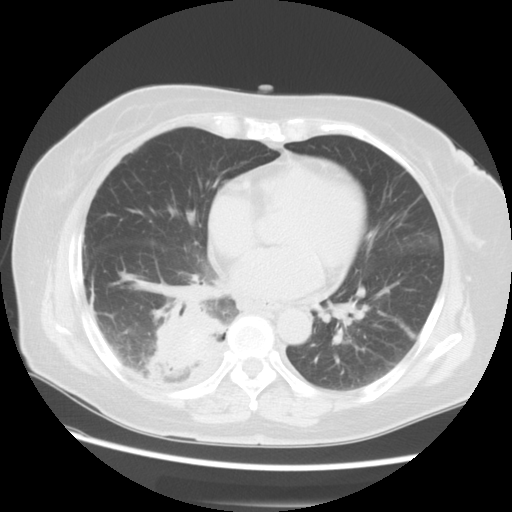
Chest CT, one axial slice; position 27 of 57 along the scan axis; 120 kVp; lung window (W 1500 / L -600 HU); 5 mm slice thickness; 512 × 512 image matrix, field of view 350 × 350 mm. Female patient, age 69 years. From the clinical record (not read from this slice): clinical TNM (as recorded): T2 N1 M1a.
Outlined on this slice (rectangle marked by the reading radiologist):
- lung tumour (recorded histology: adenocarcinoma): bounding box (x1, y1, x2, y2) in pixels: (147, 298, 225, 389)